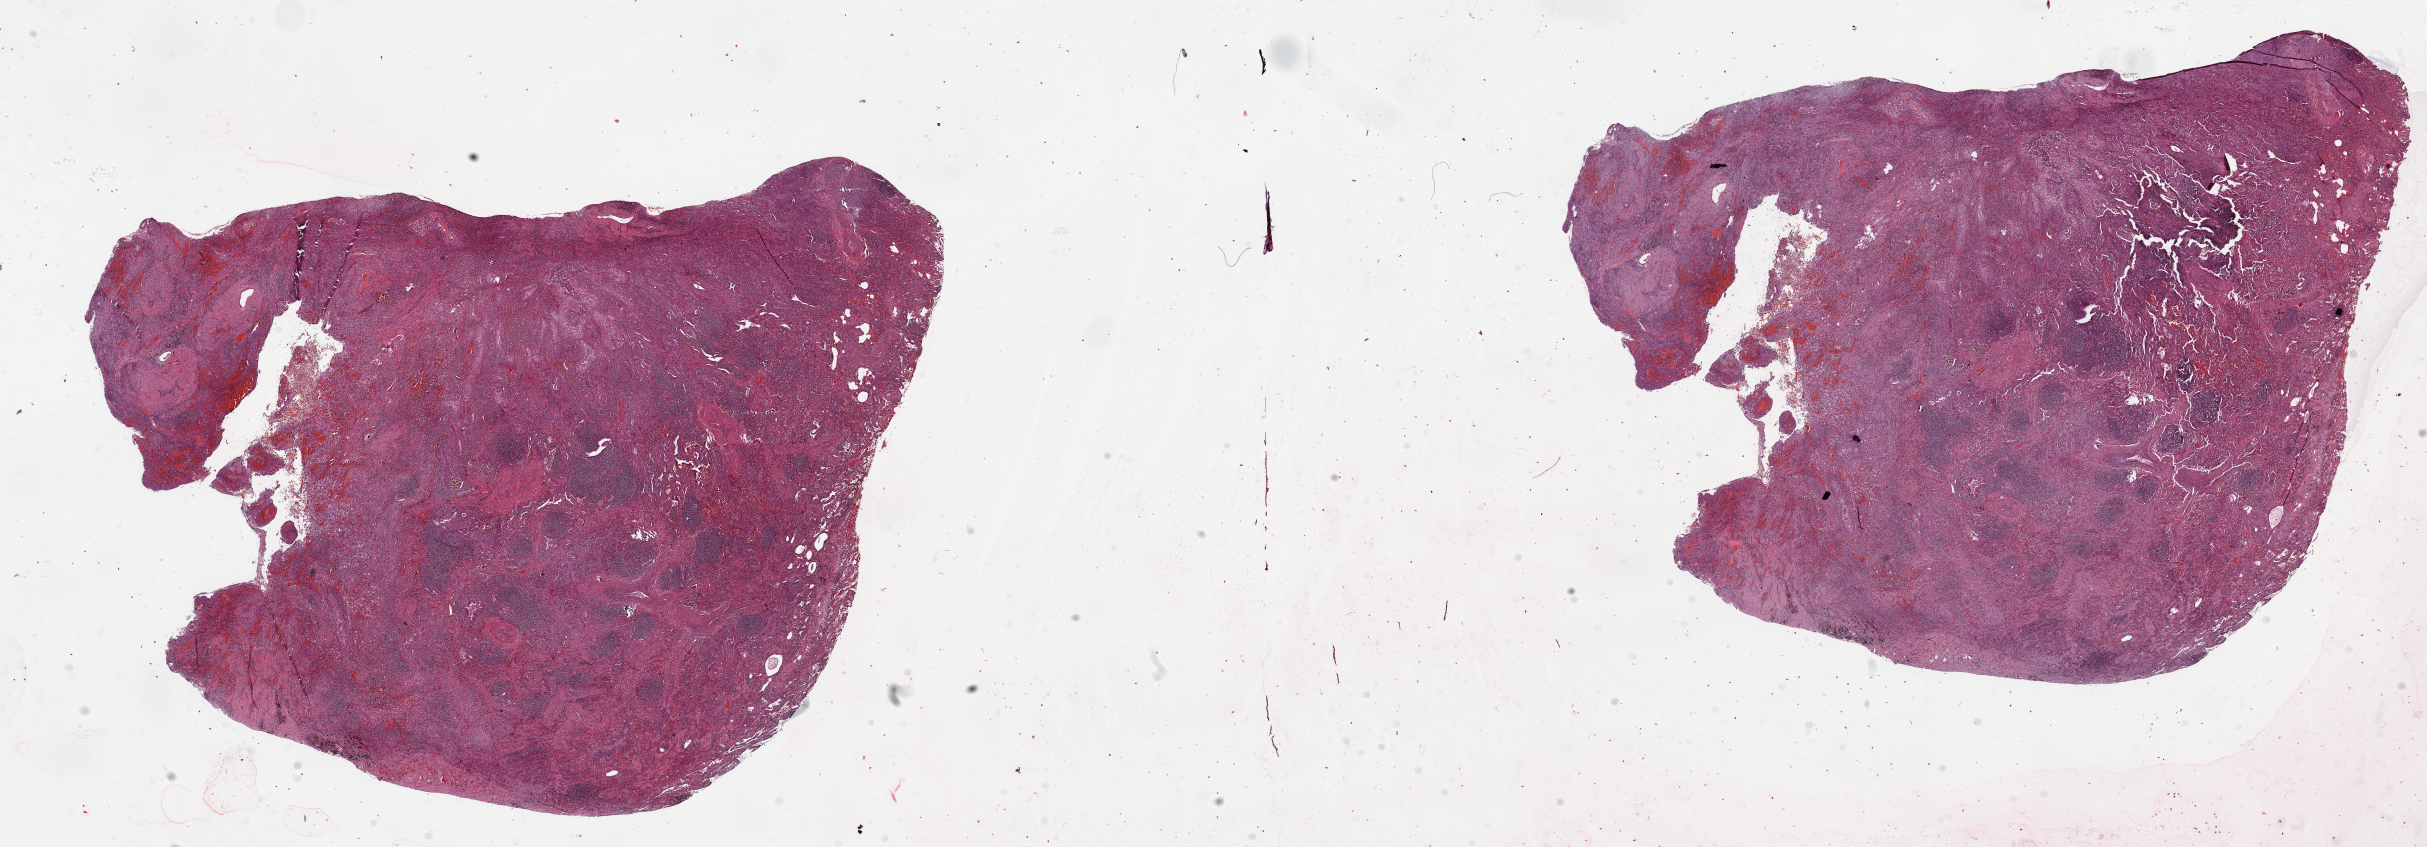
H&E-stained whole-slide image — whole scanned area (about 38.4 x 13.4 mm, acquisition: 20x scan) shown as a low-resolution overview, tumour tissue sample, lung. Patient: male, age 73 years. Histologic grade: G2 (moderately differentiated).
Histologic diagnosis: Squamous cell carcinoma, NOS. Primary tumour site (as recorded): right lower lobe. AJCC pathologic stage: IB.